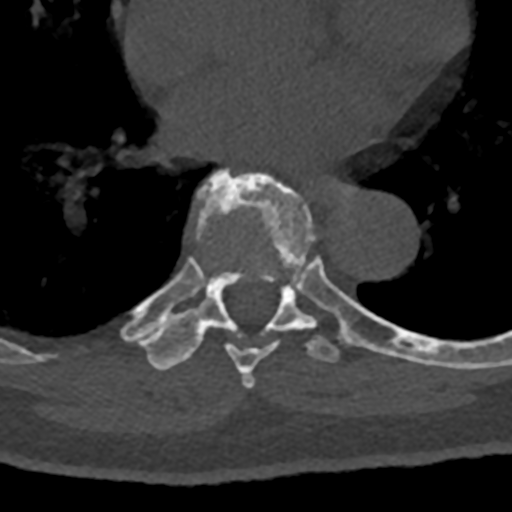
CT including the spine, one axial slice; slice 734 of 797 in the series (ordered by position); 120 kVp; bone window (W 1800 / L 400 HU); 512 × 512 image matrix, field of view 160 × 160 mm. Patient: male, 74 years. Case-level facts recorded for this patient, not image findings: primary cancer: renal; vertebrae with lytic lesions (as recorded): T10, L1, L2, L3, L4, L5.
Structures marked on this image (semi-automatic segmentation, software-assisted and operator-edited):
- T7 vertebra: box from (x=197, y=169) to (x=359, y=388) px
- T8 vertebra: (x=123, y=270)–(x=432, y=371)